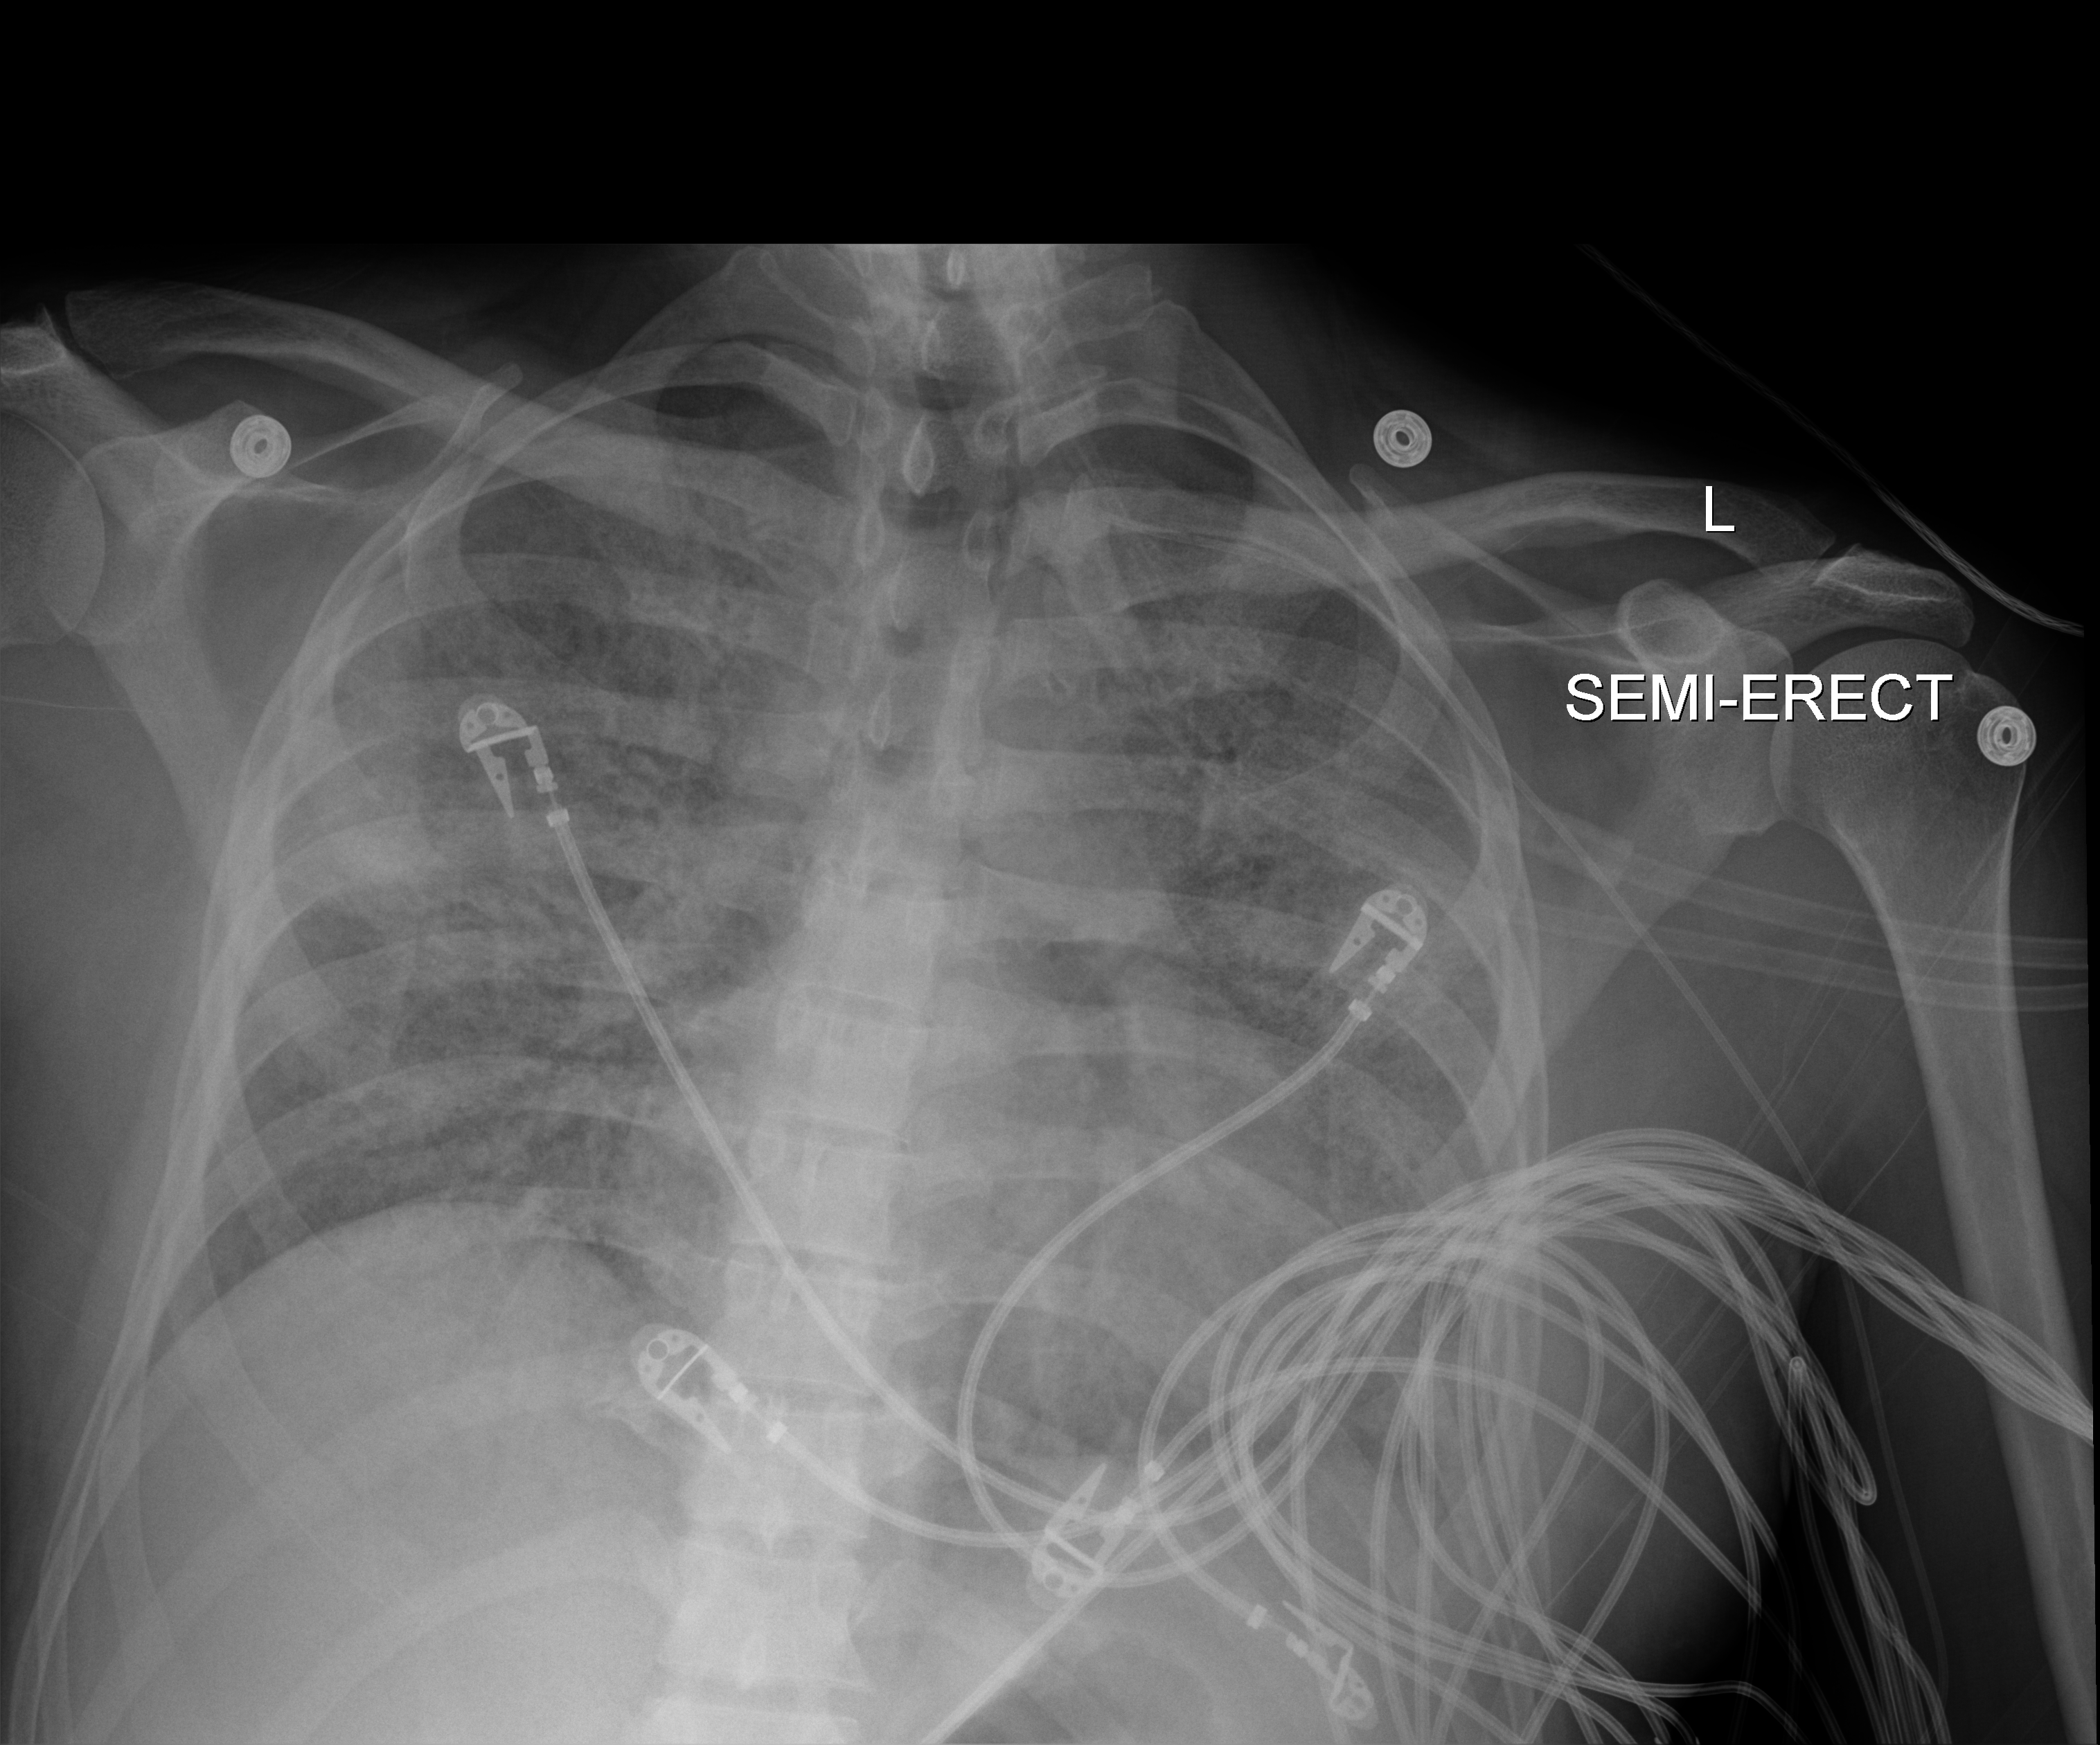
Chest X-ray (portable), anteroposterior (AP) projection. Patient hospitalised with COVID-19; male, aged 18–59 years.
From the hospital-stay record, not from the radiograph (when in the stay this image was taken is not recorded): admitted to intensive care during this hospital stay: yes; chronic kidney disease (admission record): no; length of hospital stay: 30 days.